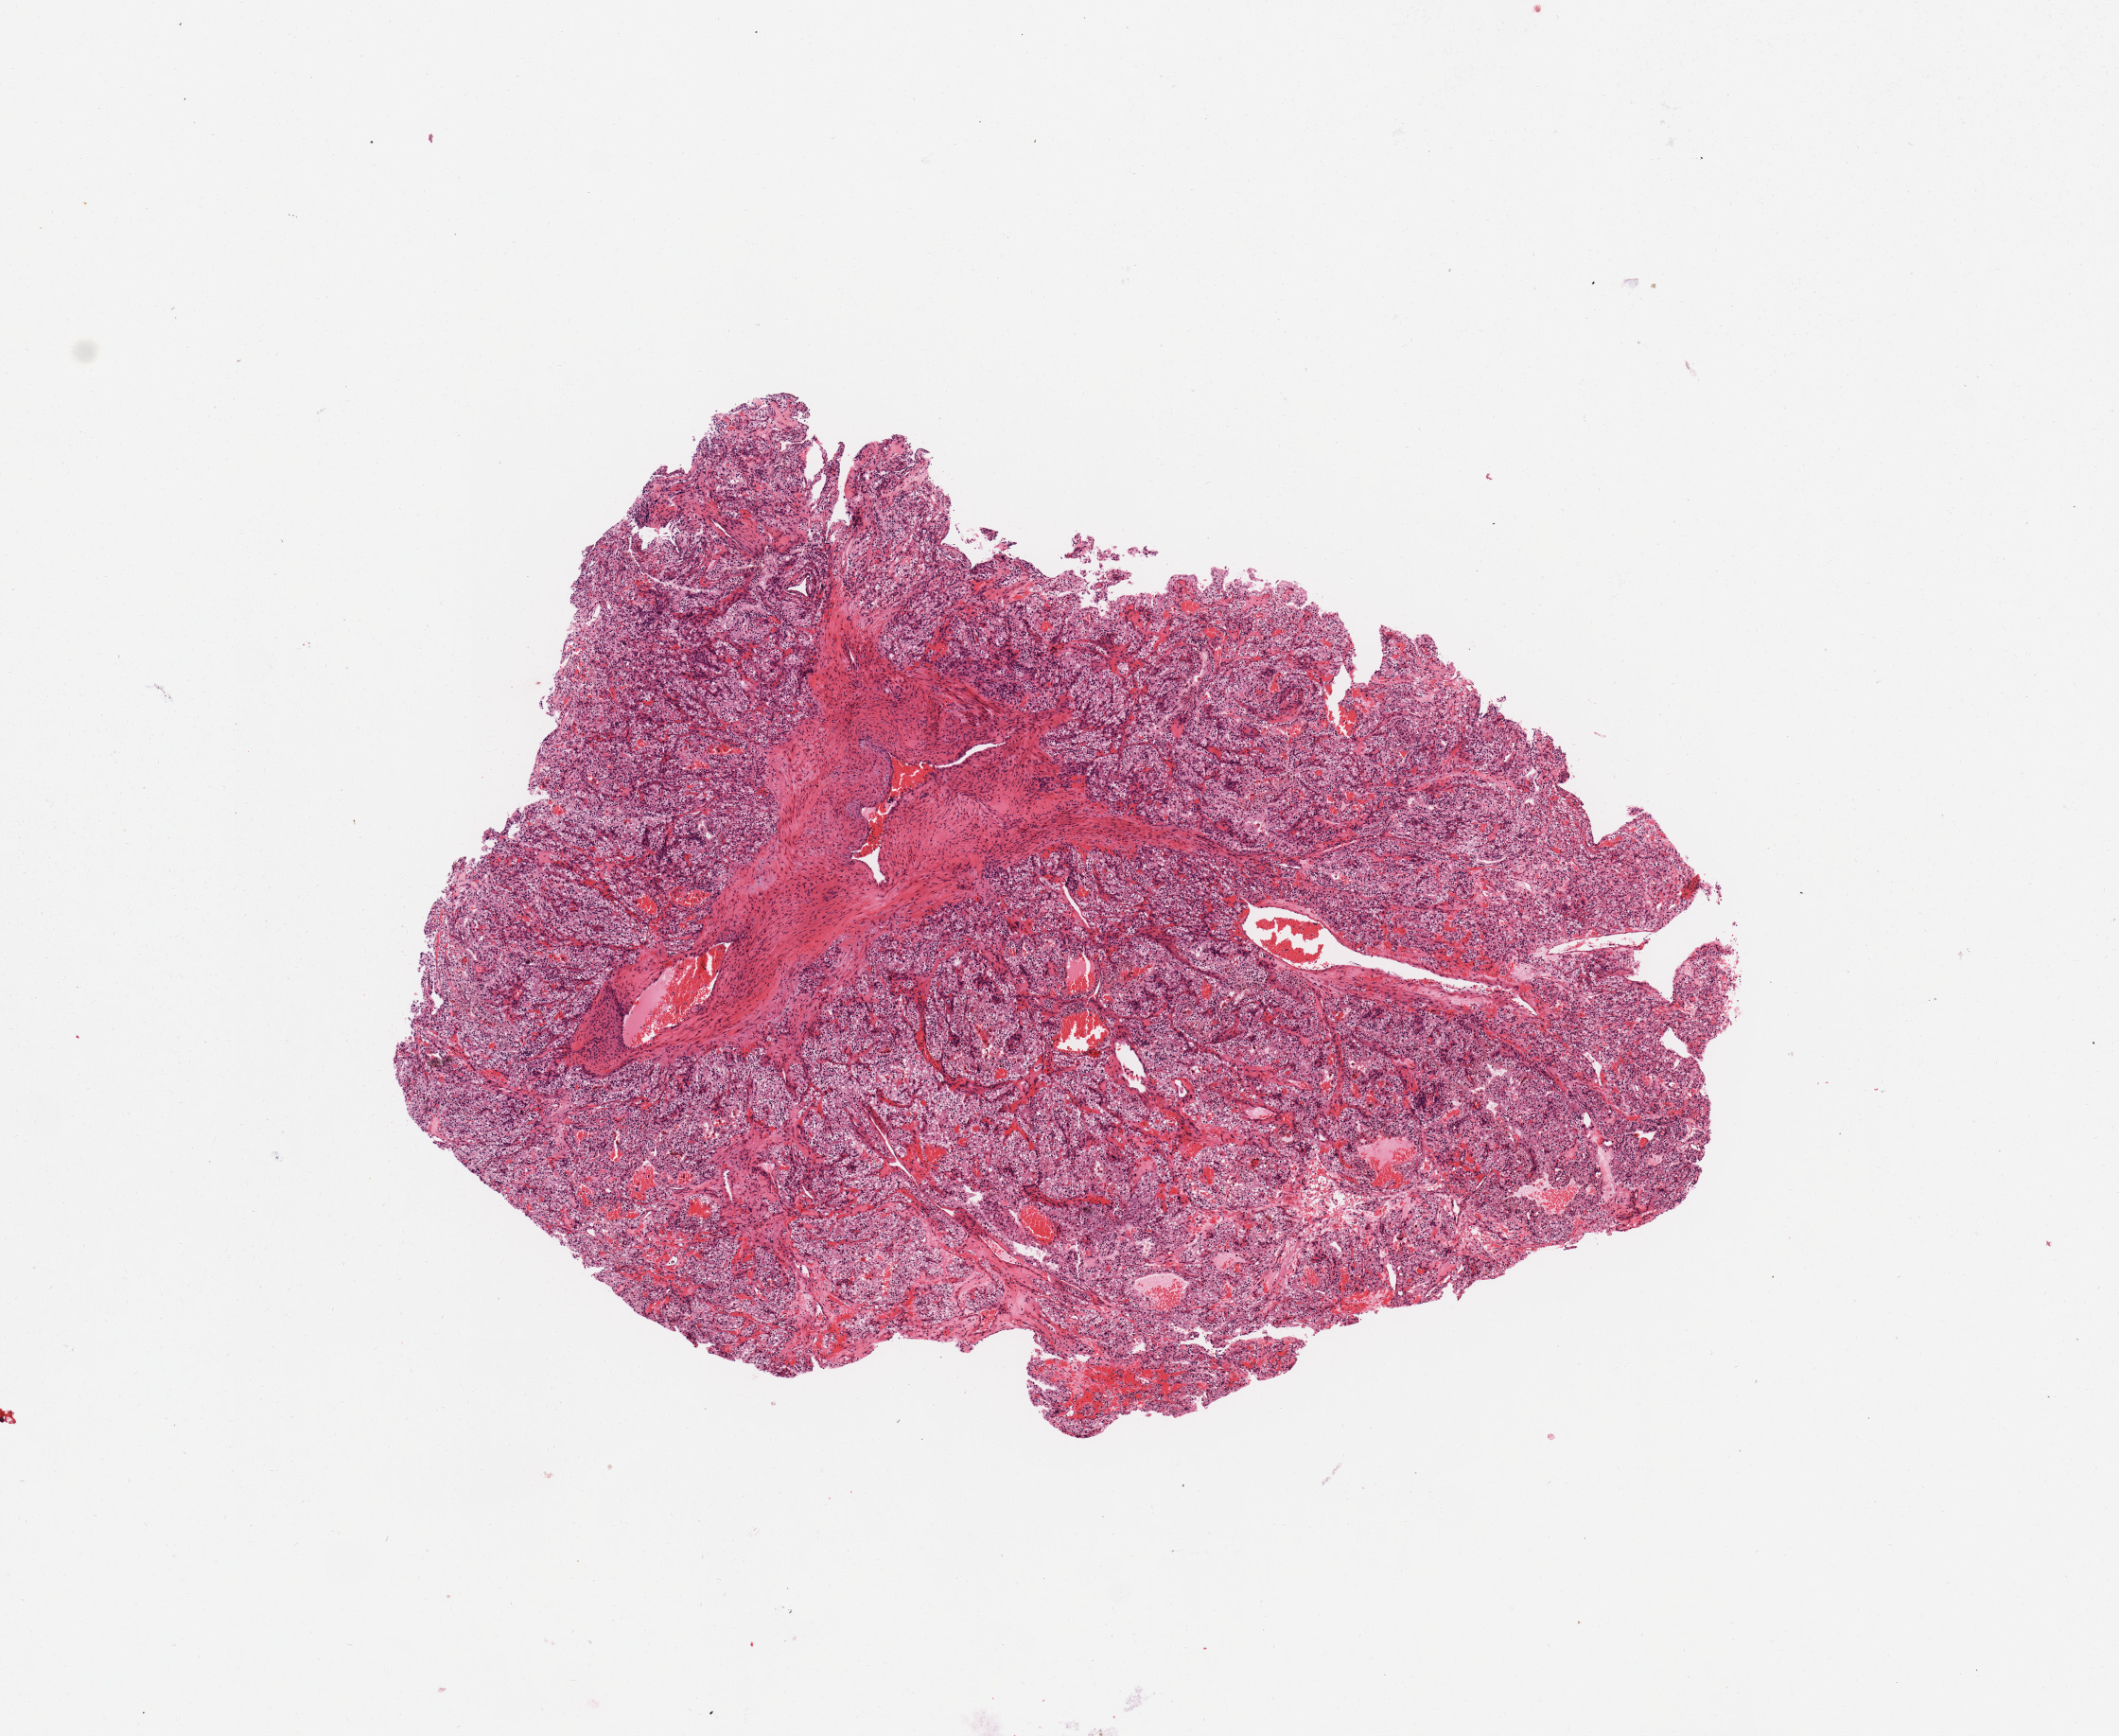
H&E whole-slide image — whole scanned area (about 8.9 x 7.3 mm, from a 20x scan) shown as a low-resolution overview, tumour tissue sample, sampled site: kidney. Male, 46 y/o. Histologic grade: G2 (moderately differentiated). Pathologist review of this section (percent, as recorded): tumour nuclei 90%, necrosis 0%.
Histologic diagnosis: Renal cell carcinoma, NOS. AJCC pathologic stage: I. Primary tumour site (as recorded): lower pole.